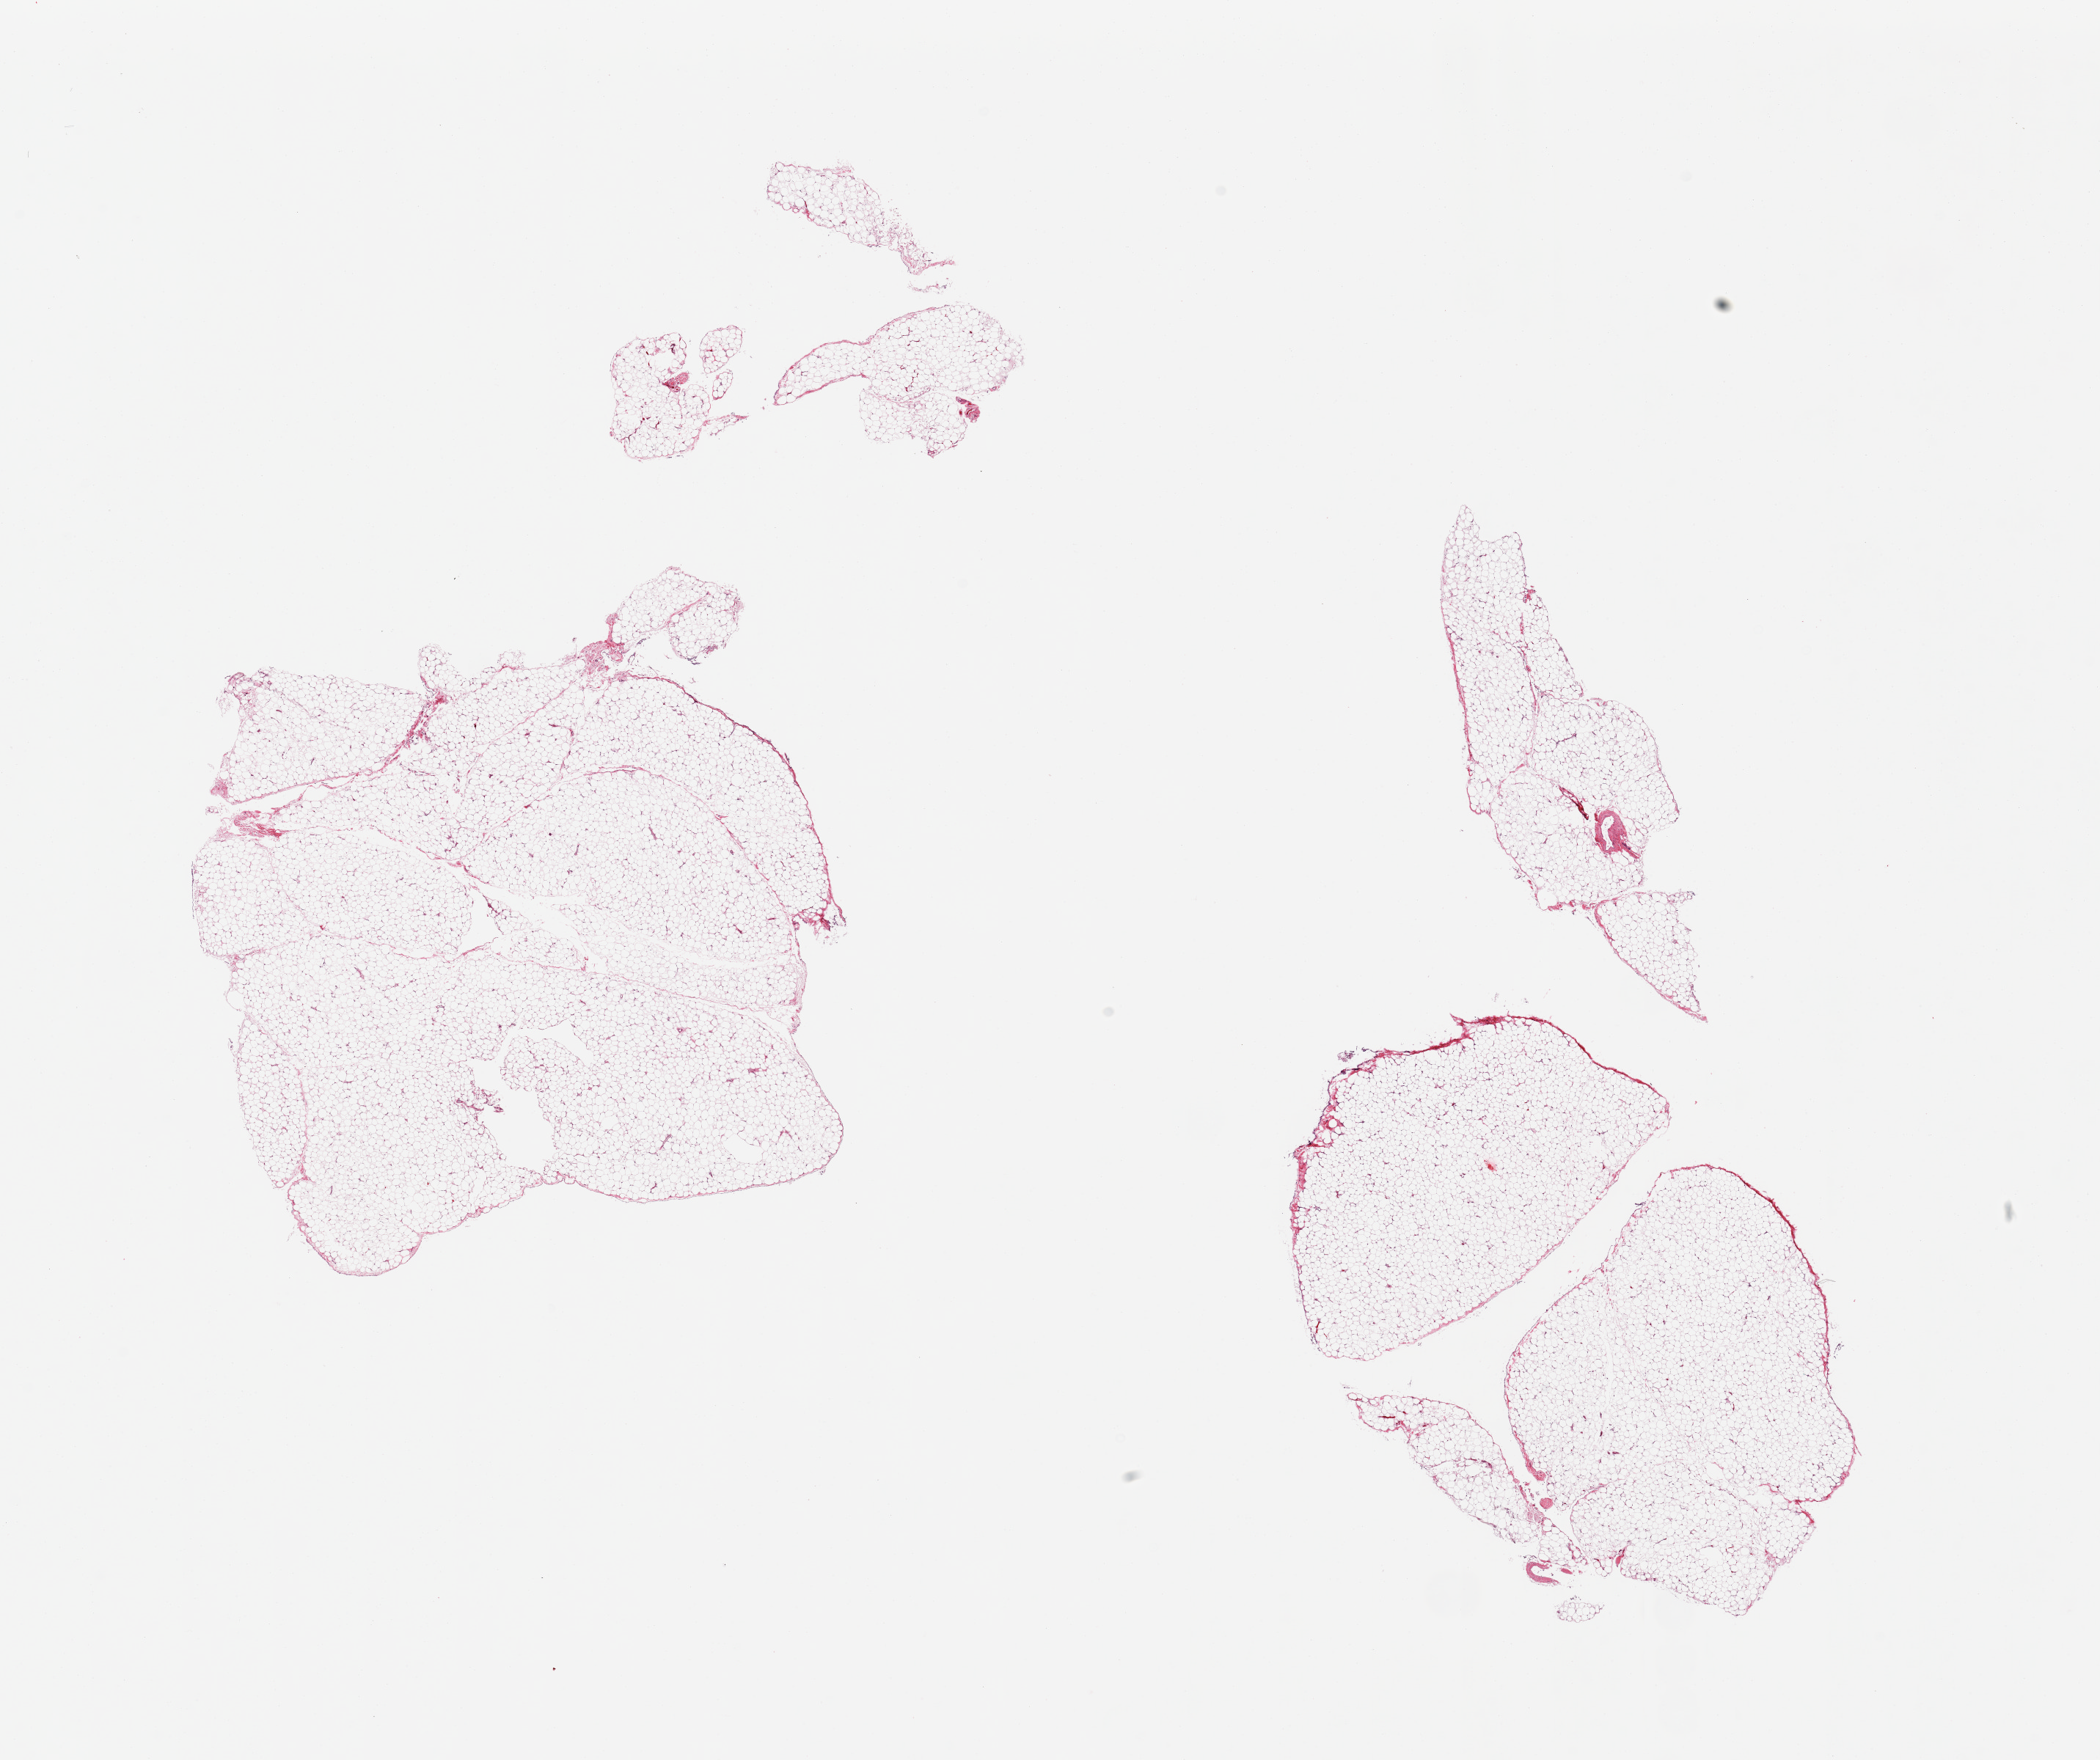
Whole-slide image, hematoxylin and eosin (H&E) stain, low-resolution overview of the scanned area, about 22.6 x 19.0 mm (from a 20x scan); PAXgene-fixed paraffin-embedded (PFPE) section; target tissue: omentum; tissue donor sample. Donor: male.
Review note (as recorded): 2 pieces, no significant vascular/fascial tissue.